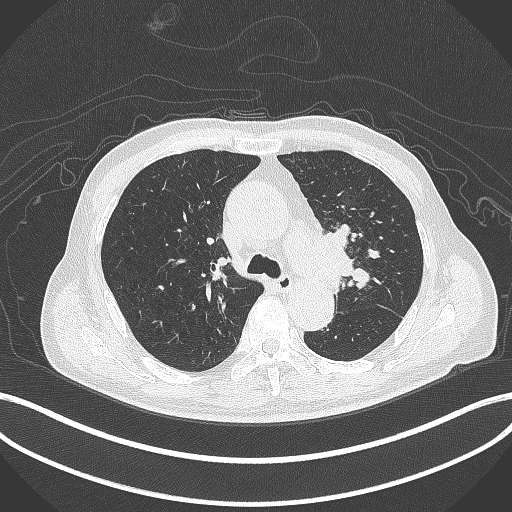
Chest CT, one axial slice; position 292 of 417 along the scan axis; reconstruction kernel B70f; 120 kVp; lung window (W 1500 / L -600 HU); 1 mm slice thickness; 512 × 512 image matrix, field of view 400 × 400 mm. Patient: male, 77 years. Case-level facts recorded for this patient, not image findings: clinical TNM (as recorded): T3 N1 M0.
Outlined on this slice (bounding box drawn by a radiologist):
- lung tumour (recorded histology: adenocarcinoma): bounding box <314,226,353,288> (left, top, right, bottom; pixels)